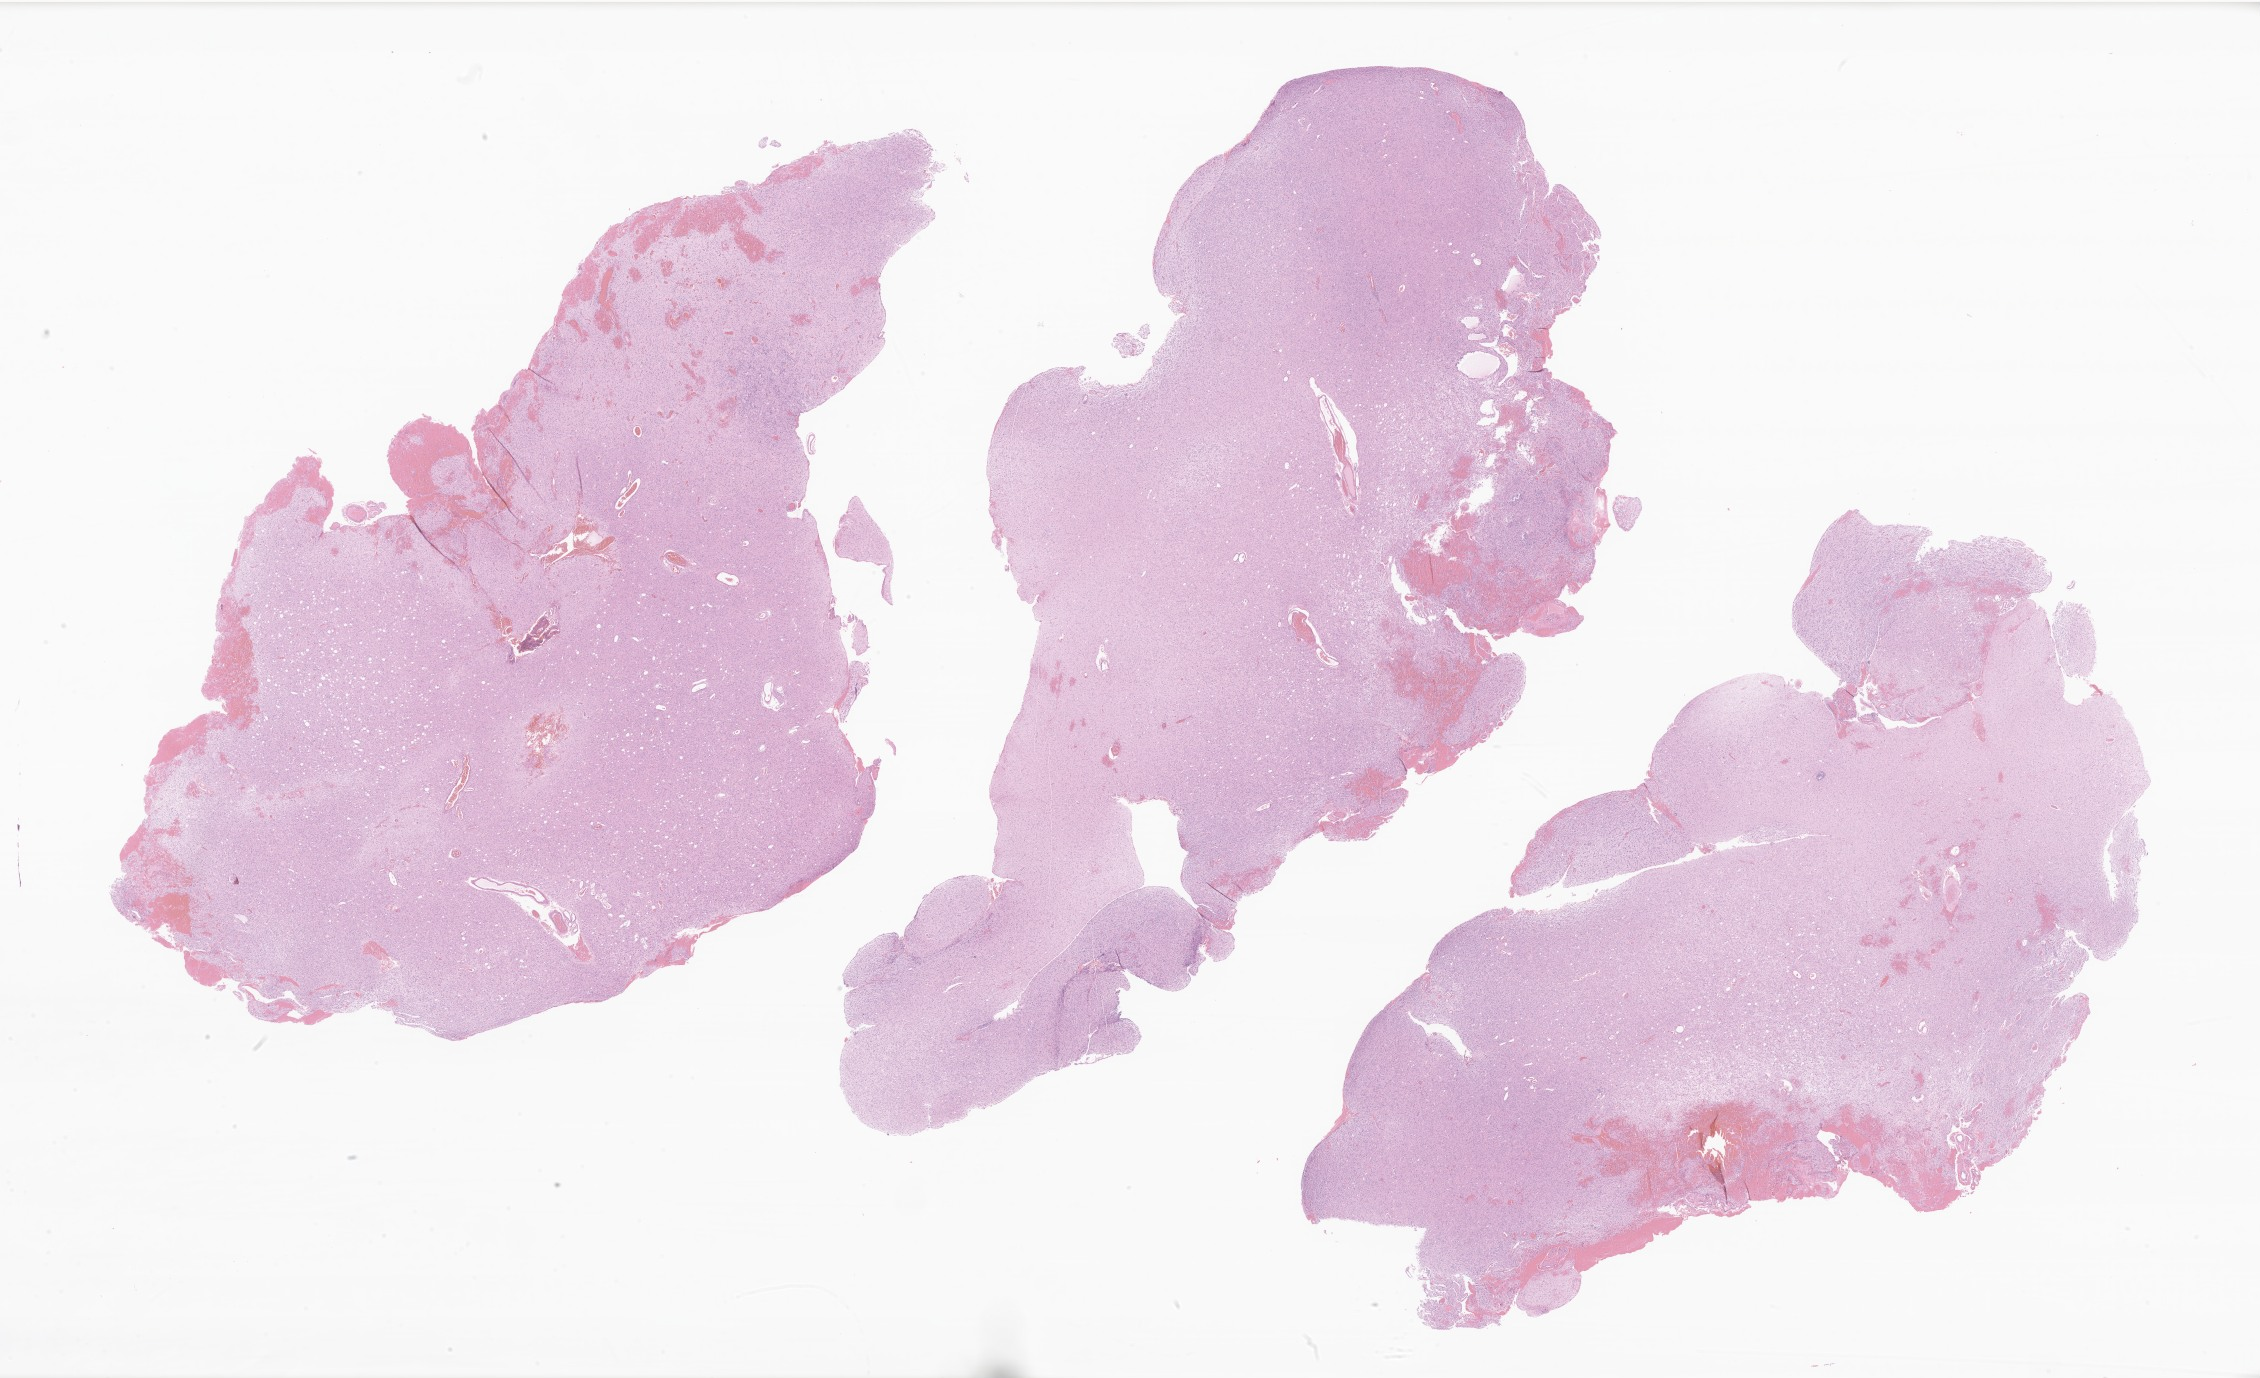
Digitized H&E-stained section of tumor tissue from the brain — a low-resolution overview of the entire scanned area, about 38.1 x 23.2 mm. Formalin-fixed paraffin-embedded section. Male patient, age 272 months (22 years 8 months).
Diagnosis (ICD-O-3 morphology term): Astrocytoma, NOS.